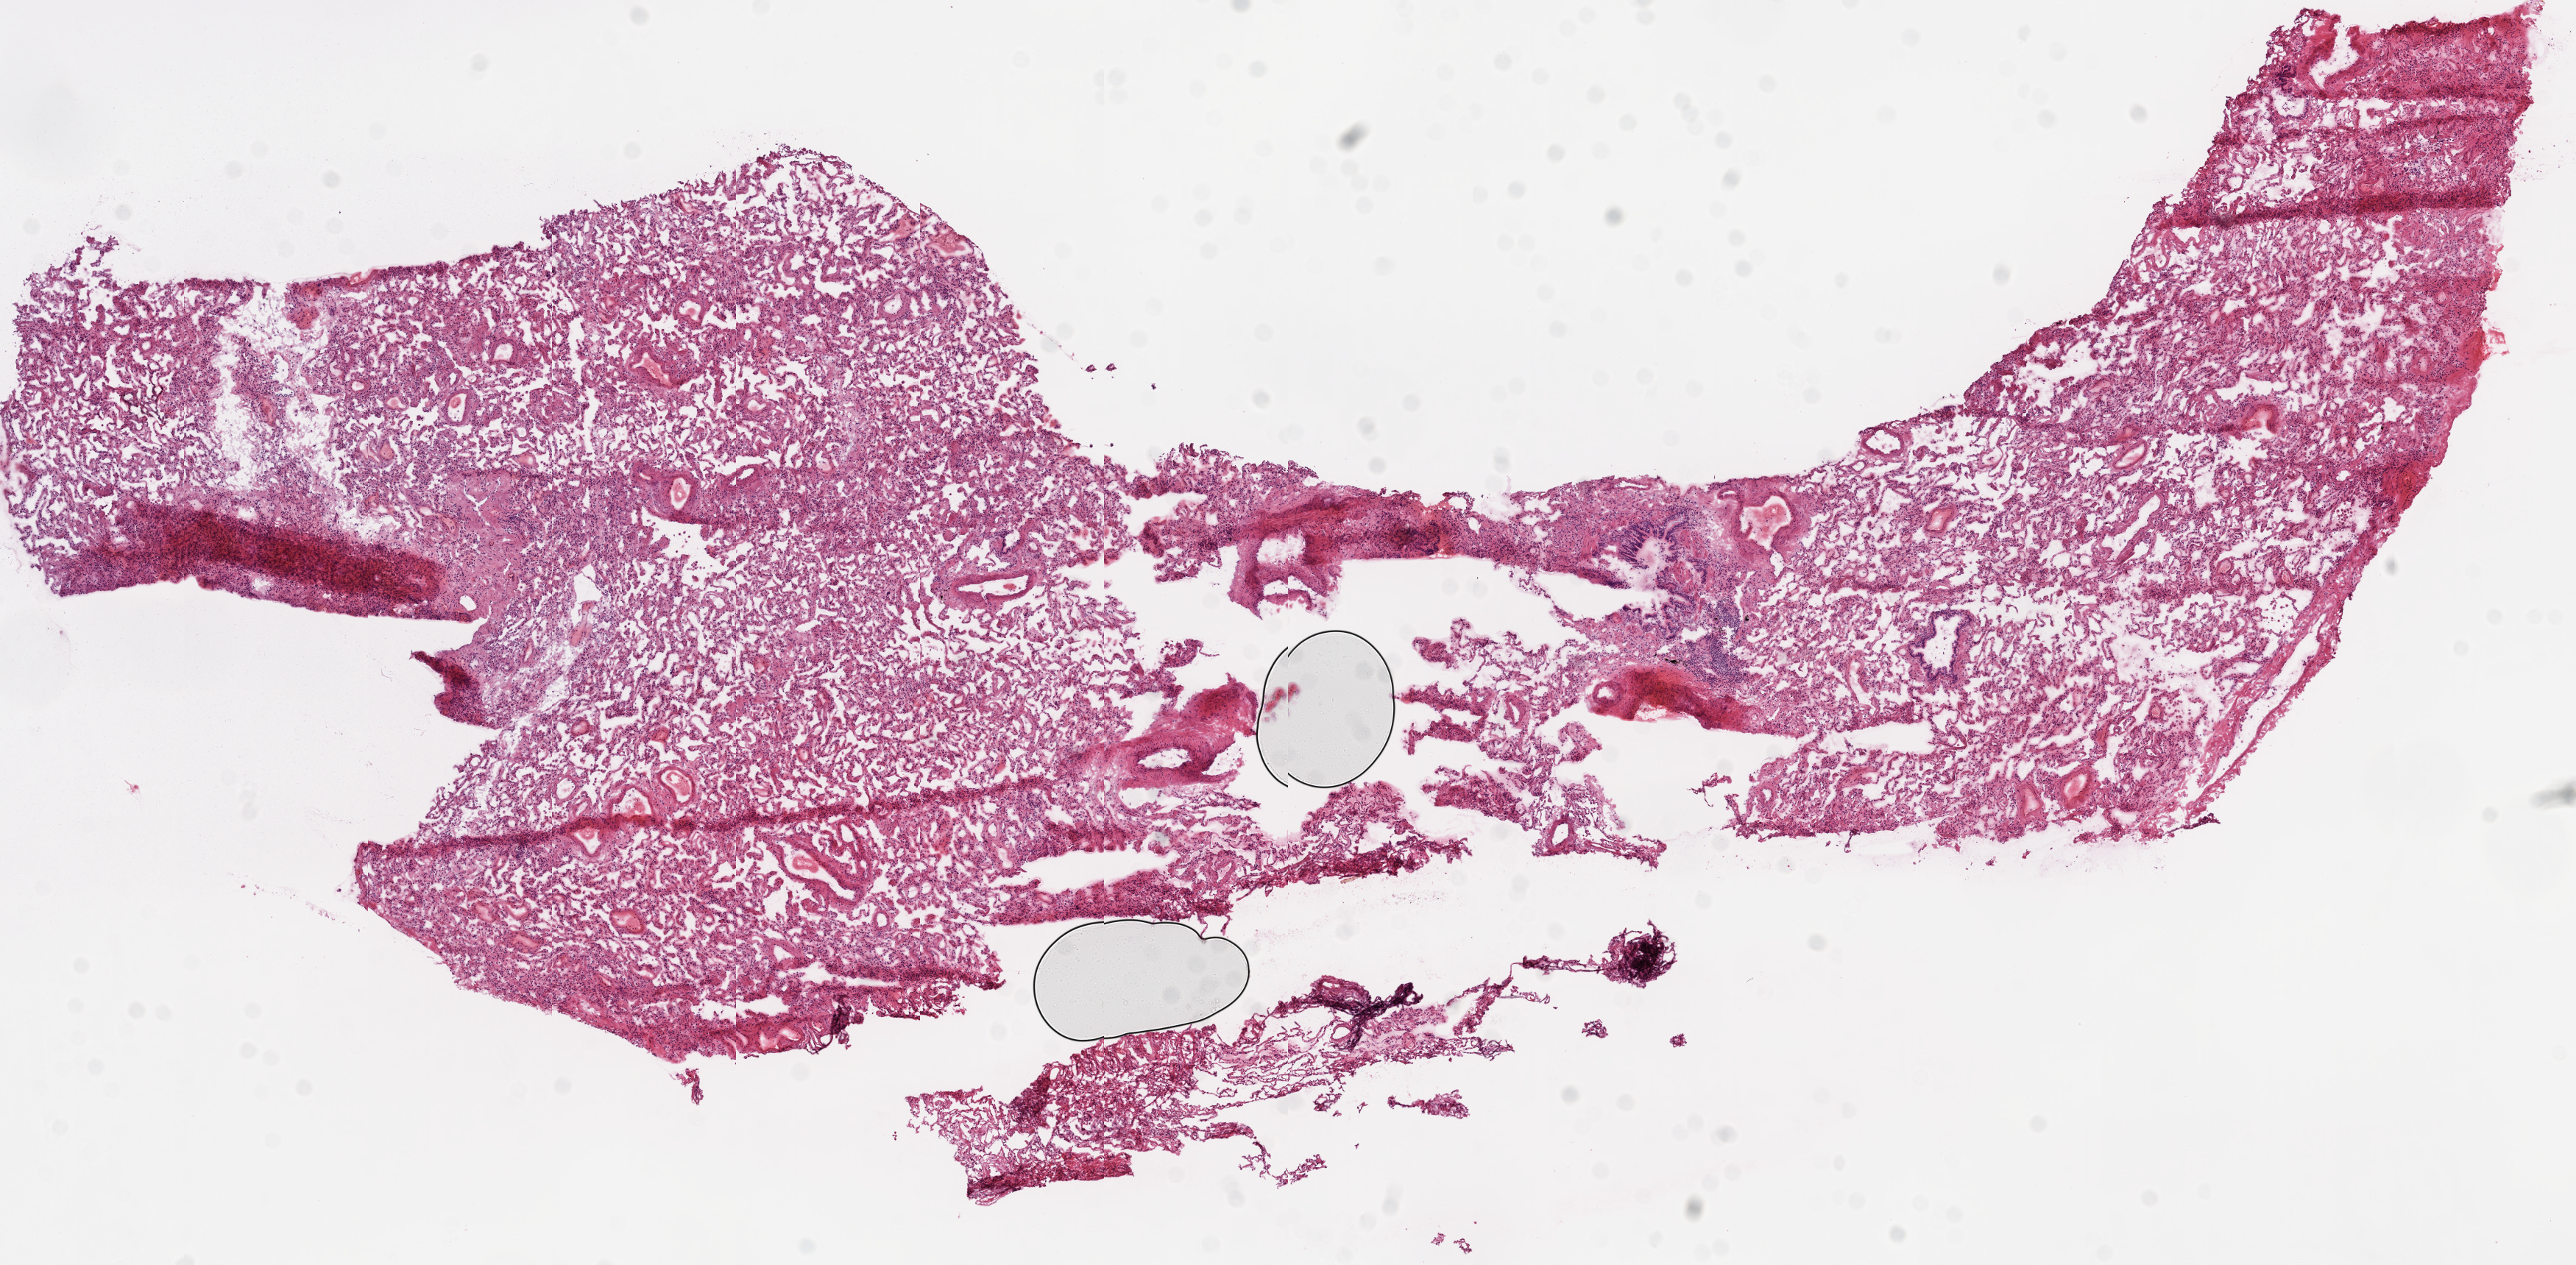
H&E-stained whole-slide image — a low-resolution overview of the entire scanned area, about 14.0 x 6.9 mm. Frozen section from the top of the tissue portion. Sample: solid tissue normal (non-tumour tissue), lung. Male patient; age at initial diagnosis 68 years.
This section: solid tissue normal (non-tumour) sample from the same patient. Patient diagnosis: Squamous cell carcinoma, NOS (upper lobe, lung).